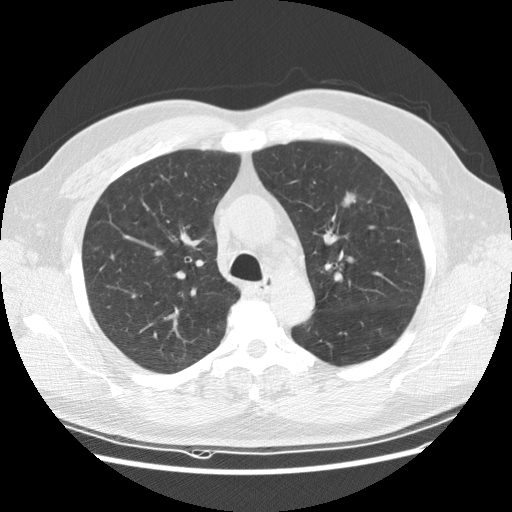
Low-dose screening chest CT, axial slice. Baseline annual screen. Lung window (W 1500 / L -600 HU). Standard (soft-tissue) reconstruction kernel (STANDARD). Slice 43 of 152 in the series. Male participant, aged 65 years at enrolment.
- Expert reader's lesion annotation, bounding box (x1, y1, x2, y2) in pixels: (325, 181, 378, 226).
- The screening reader recorded 2 non-calcified nodules or masses ≥4 mm on this exam (left upper lobe, right upper lobe); which of them this box marks is not recorded.
- Lung cancer was diagnosed 488 days after this screen: carcinoma, NOS, left upper lobe, poorly differentiated (G3), stage IIIA (AJCC 6th edition), 25 mm at pathology.